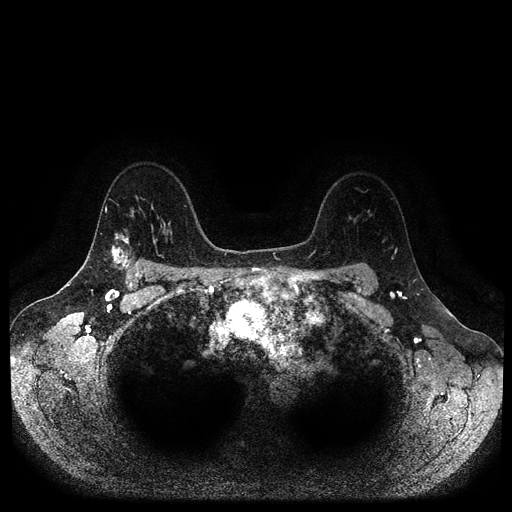
Breast MRI (dynamic contrast-enhanced, multi-phase), one axial slice; slice 75 of 116 in the series (ordered by position); dynamic contrast-enhanced series, time point 2 of 5 at this slice position (early post-contrast); 1.5 T; TE 2.6 ms, TR 5.3 ms; 512 × 512 image matrix, field of view 360 × 360 mm. Patient: female, 45 years.
Structures marked on this image (semi-automatically segmented with operator editing):
- breast lesion (labelled 'tumour' in the annotation; benign lesions carry a separate 'benign' label): box from (x=109, y=243) to (x=133, y=271) px